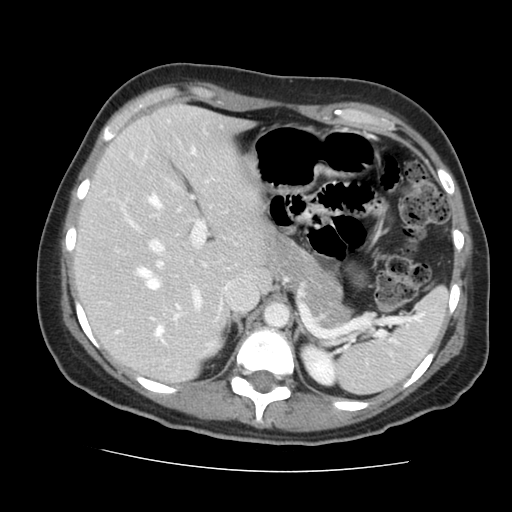
Contrast-enhanced abdominal CT, one axial slice; slice 101 of 144 in the series (ordered by position); intravenous contrast given; soft-tissue window (W 400 / L 40 HU); 2.5 mm slice thickness; 512 × 512 image matrix, field of view 333 × 333 mm. Female patient, age 46 years. Case-level facts recorded for this patient, not image findings: diagnosis: colorectal cancer liver metastases, imaged before liver resection; multiple liver metastases: no; largest metastasis: 2.8 cm; disease in both lobes: no.
Annotated regions visible in this slice (outlined manually by an expert reader):
- hepatic veins: bounding box [x1, y1, x2, y2] px = [145, 196, 161, 289]
- liver: [78, 105, 271, 381]
- planned liver remnant (the part of the liver to remain after resection): [78, 105, 271, 381]
- portal vein (with intrahepatic branches): [116, 196, 206, 337]